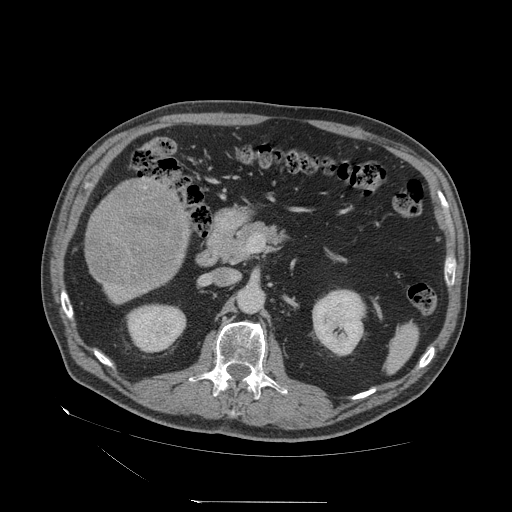
Contrast-enhanced abdominal CT (liver protocol), one axial slice. Slice 13 of 83 in the series (ordered by position). Reconstruction kernel STANDARD. 140 kVp. Soft-tissue window (W 400 / L 40 HU). 2.5 mm slice thickness. 512 × 512 image matrix, field of view 460 × 460 mm. From the clinical record (not read from this slice): diagnosis: hepatocellular carcinoma (patient treated with transarterial chemoembolisation; whether this scan precedes or follows treatment is not stated here); TNM stage (as recorded): Stage-I; Child-Pugh class: A; tumour differentiation: well differentiated; tumour nodularity: uninodular.
Annotated regions visible in this slice (semi-automatic segmentation, software-assisted and operator-edited):
- liver parenchyma outside the tumour (the mass and vessels are separate outlines, so this box may not span the whole liver): bounding box (x1, y1, x2, y2) in pixels: (98, 180, 188, 302)
- mass: (88, 182, 187, 285)